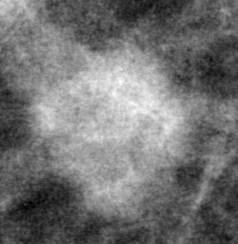
Crop from a digitized film mammogram around one marked abnormality; left breast; CC view.
Finding: mass, shape oval, margins spiculated; BI-RADS assessment category 4; pathology result (as recorded, not read from the image): malignant.